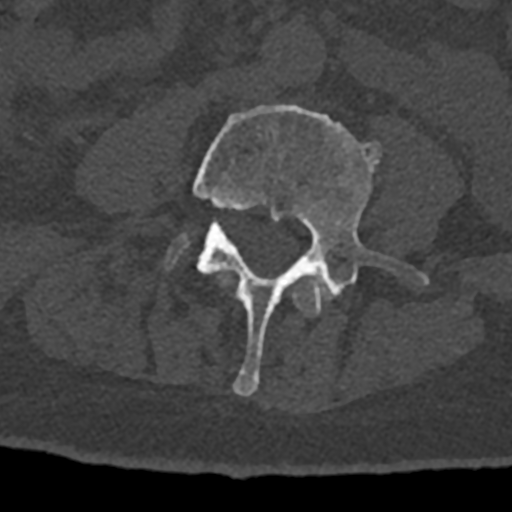
CT including the spine, one axial slice; position 262 of 797 along the scan axis; 120 kVp; bone window (W 1800 / L 400 HU); 512 × 512 image matrix, field of view 160 × 160 mm. Male patient, age 74 years. From the clinical record (not read from this slice): primary cancer: renal; vertebrae with lytic lesions (as recorded): T10, L1, L2, L3, L4, L5.
Outlined on this slice (semi-automatically segmented with operator editing):
- L3 vertebra: box from (x=214, y=271) to (x=332, y=316) px
- L4 vertebra: (x=190, y=105)–(x=429, y=396)
- L5 vertebra: (x=169, y=235)–(x=187, y=264)